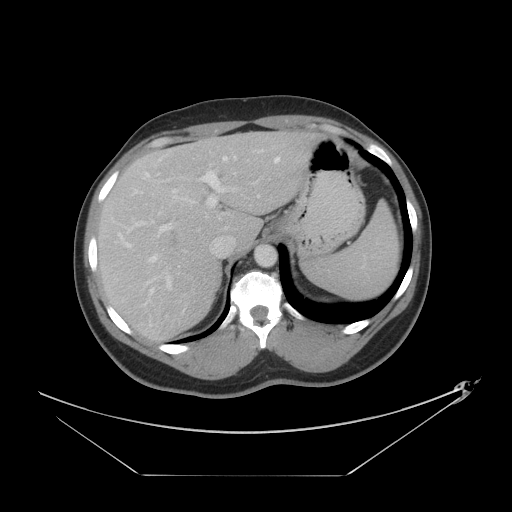
Contrast-enhanced abdominal CT, one axial slice; position 30 of 44 along the scan axis; soft-tissue window (W 400 / L 40 HU); 512 × 512 image matrix. Male patient, age 49 years. Case-level facts recorded for this patient, not image findings: diagnosis: colorectal cancer liver metastases, imaged before liver resection; multiple liver metastases: no; largest metastasis: 8.5 cm; chemotherapy before resection: yes.
Outlined on this slice (expert manual segmentation):
- hepatic veins: bounding box <141,156,280,262> (left, top, right, bottom; pixels)
- liver: <98,131,322,340>
- planned liver remnant (the part of the liver to remain after resection): <185,131,322,247>
- portal vein (with intrahepatic branches): <118,160,237,288>
- liver metastasis: <168,230,178,247>